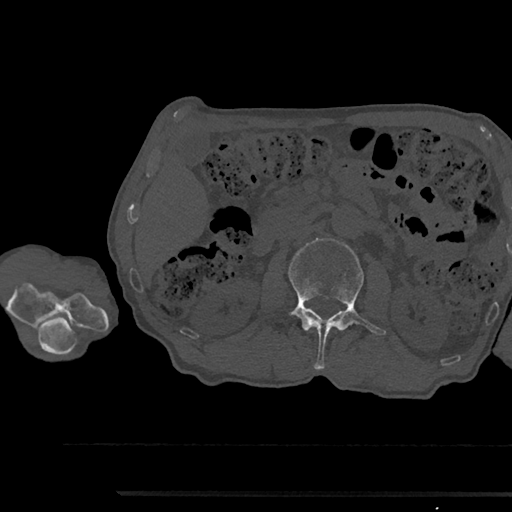
CT including the spine, one axial slice; slice 564 of 797 in the series (ordered by position); reconstruction kernel Br40s/3; 120 kVp; bone window (W 1800 / L 400 HU); 0.5 mm slice thickness; 512 × 512 image matrix, field of view 367 × 367 mm. Patient: male, 79 years. From the clinical record (not read from this slice): primary cancer: prostate.
Annotated regions visible in this slice (semi-automatically segmented with operator editing):
- L2 vertebra: box from (x=287, y=238) to (x=385, y=369) px